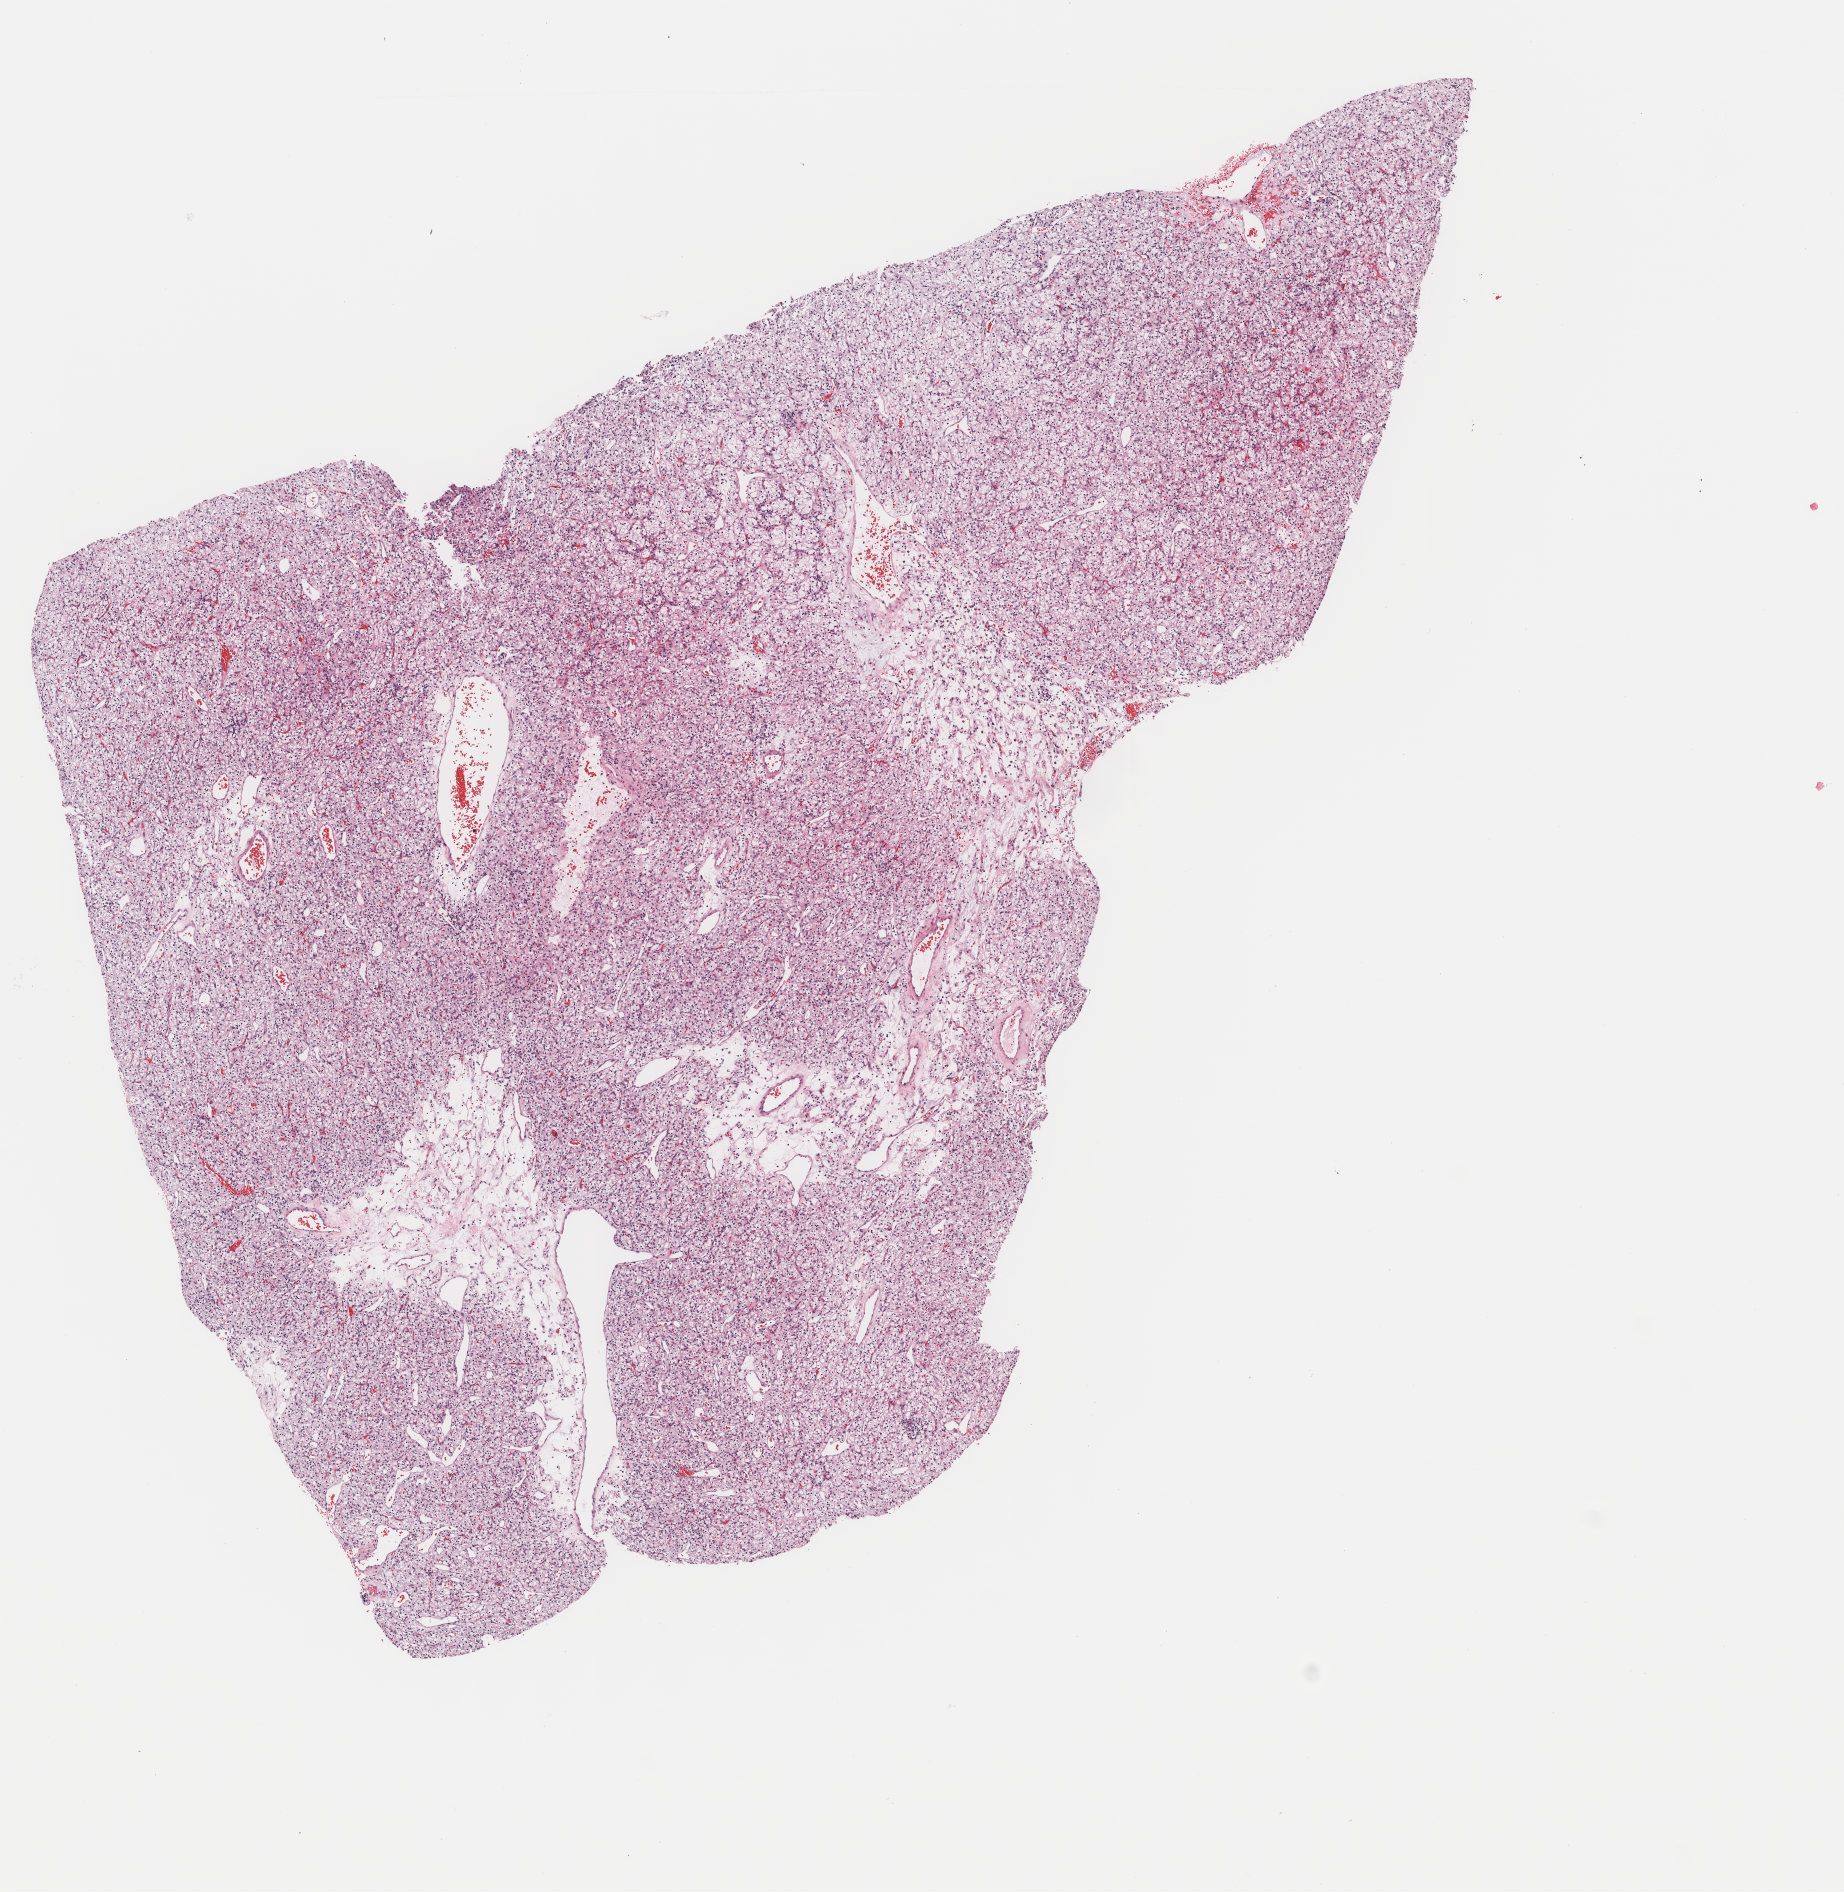
H&E whole-slide image, shown as a low-resolution overview of the whole scanned area (about 7.3 x 7.5 mm, acquisition: 40x scan). Frozen section. Kidney, primary tumour sample. Male, age 74 years at initial diagnosis. Histologic grade: G2 (moderately differentiated). Composition of this section per pathologist review: tumour cells 78%, tumour nuclei 90%, normal cells 0%, stromal cells 22%, necrosis 0%. Infiltration values recorded for this section: lymphocyte infiltration 4%, monocyte infiltration 1%, neutrophil infiltration 1%.
Pathologic diagnosis: Clear cell adenocarcinoma, NOS. AJCC pathologic stage: I. TNM: T1a NX M0.